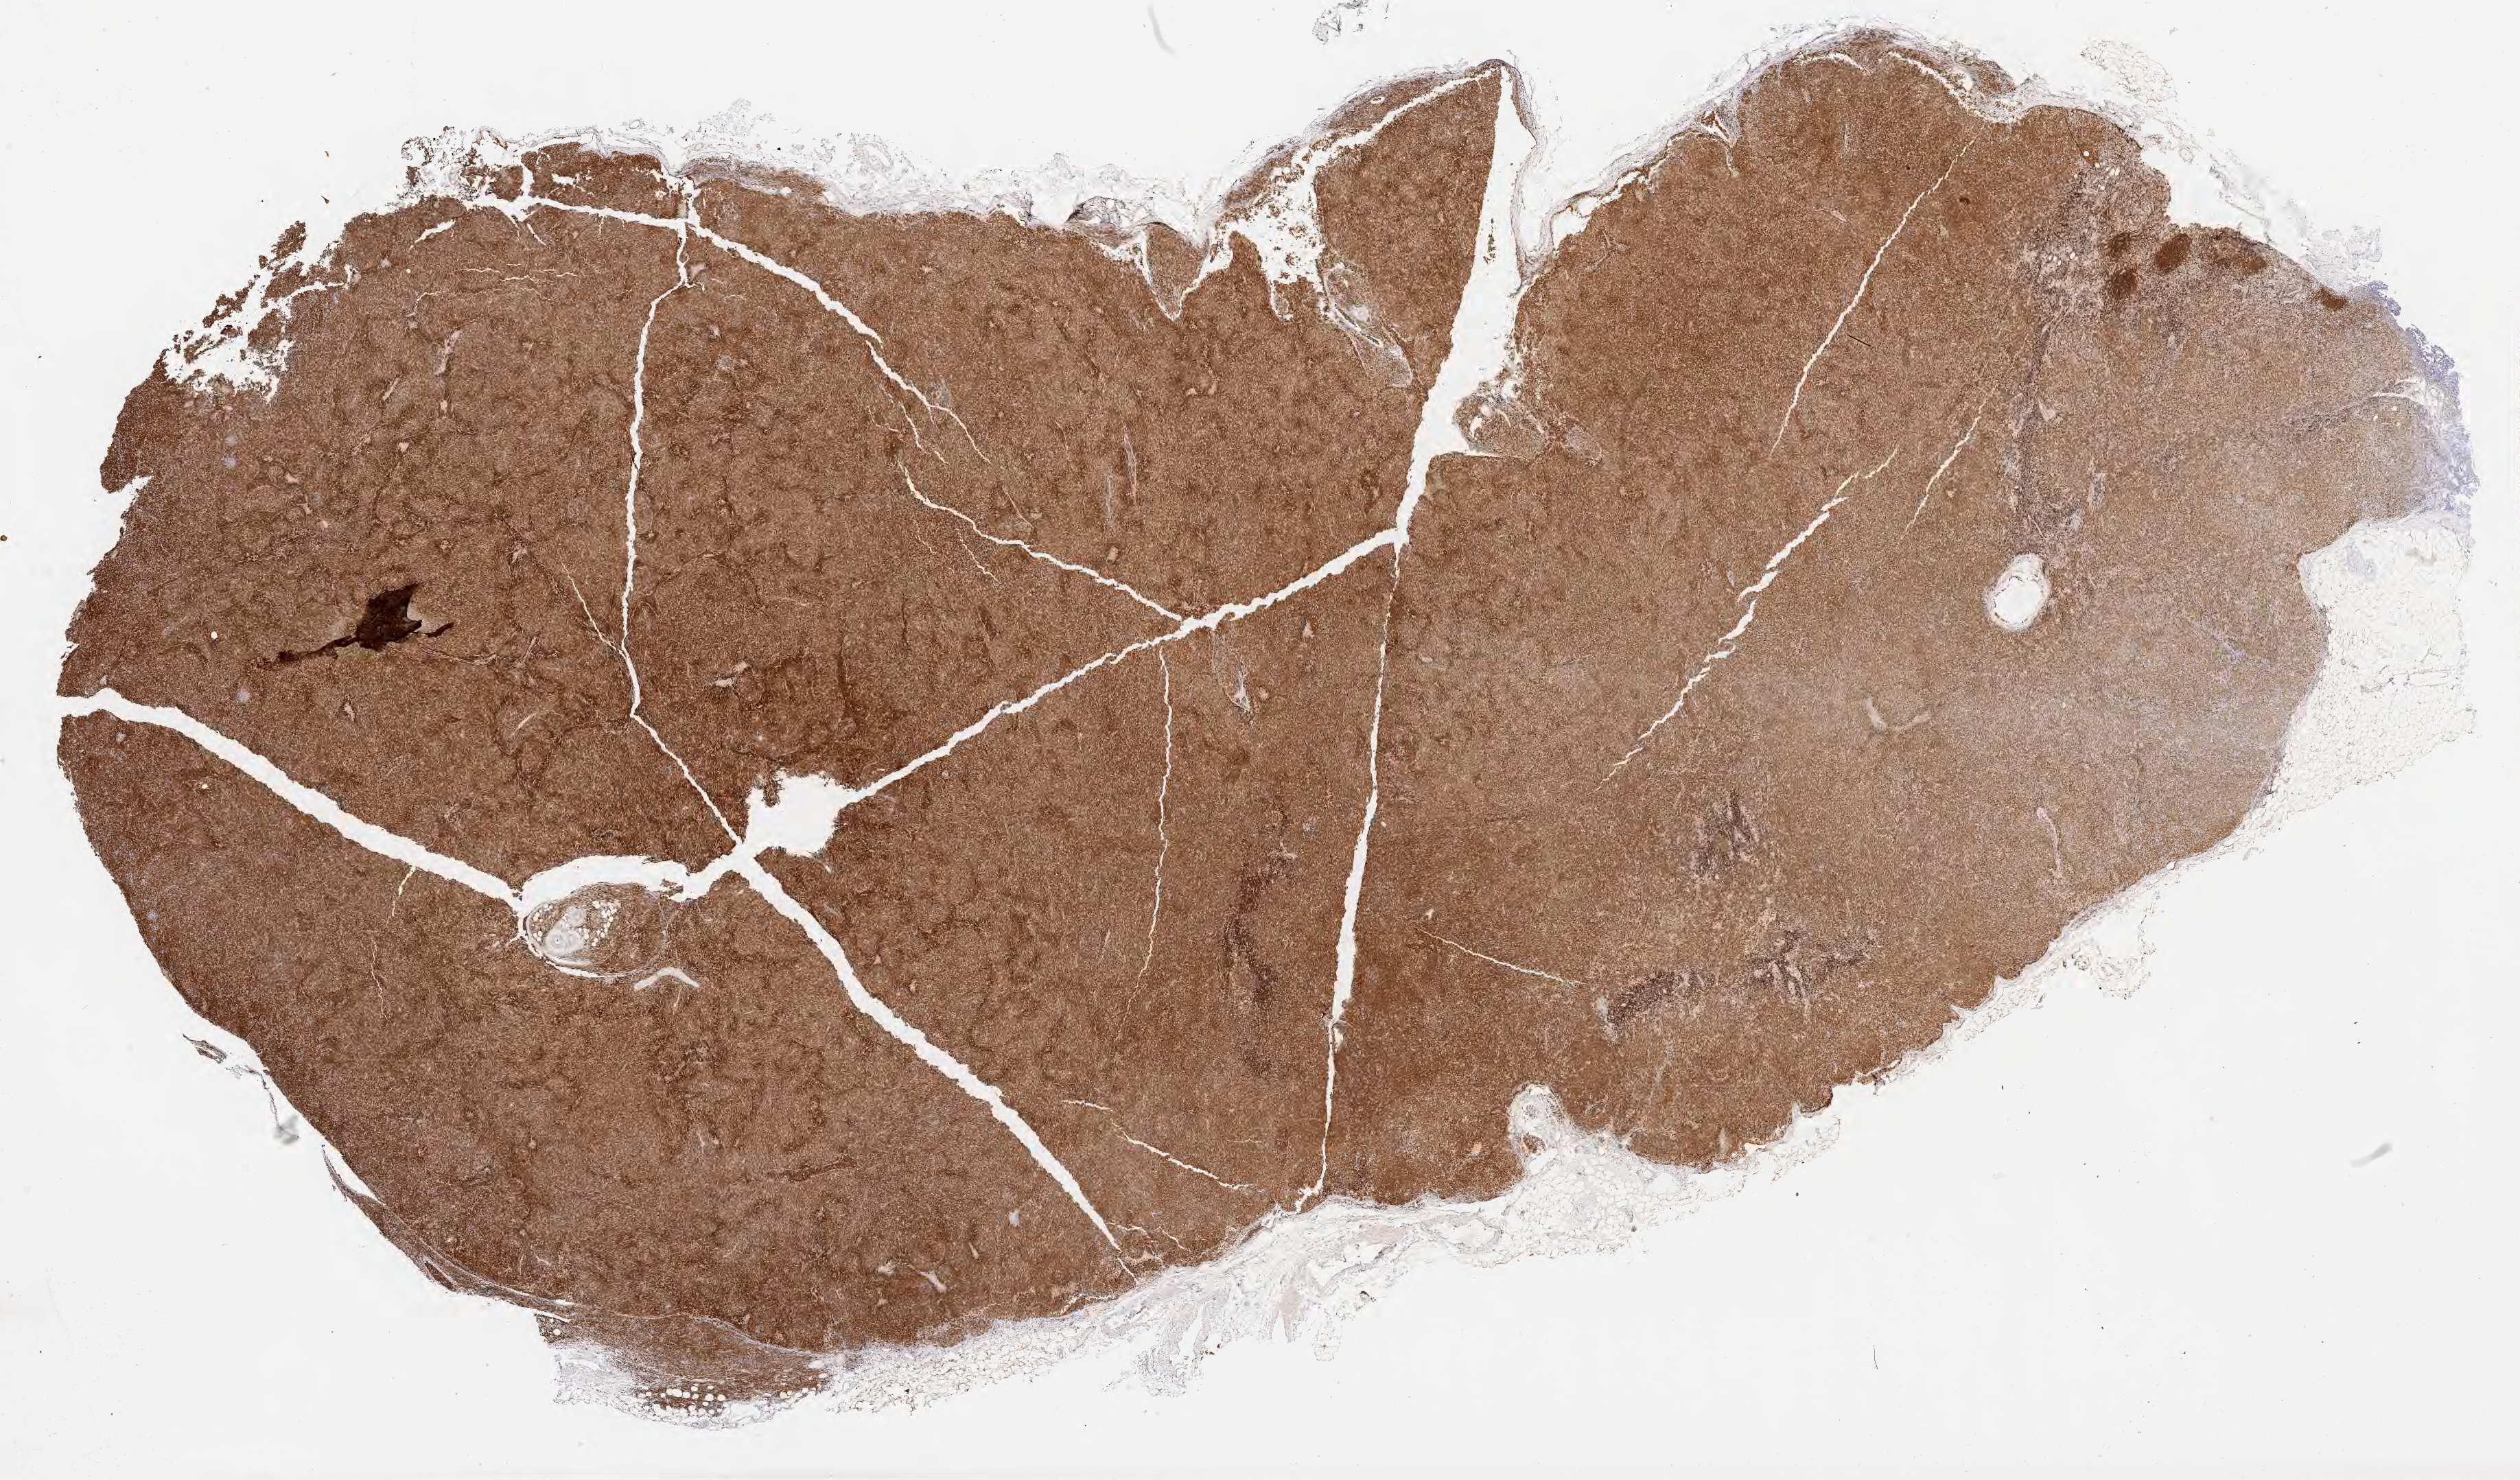
Whole-slide image, immunohistochemical stain for BCL2 — shown as a low-resolution overview of the whole scanned area (about 29.7 x 17.4 mm); tumor tissue. Patient male; aged 69.
Diagnosis: Diffuse large B-cell lymphoma, NOS.